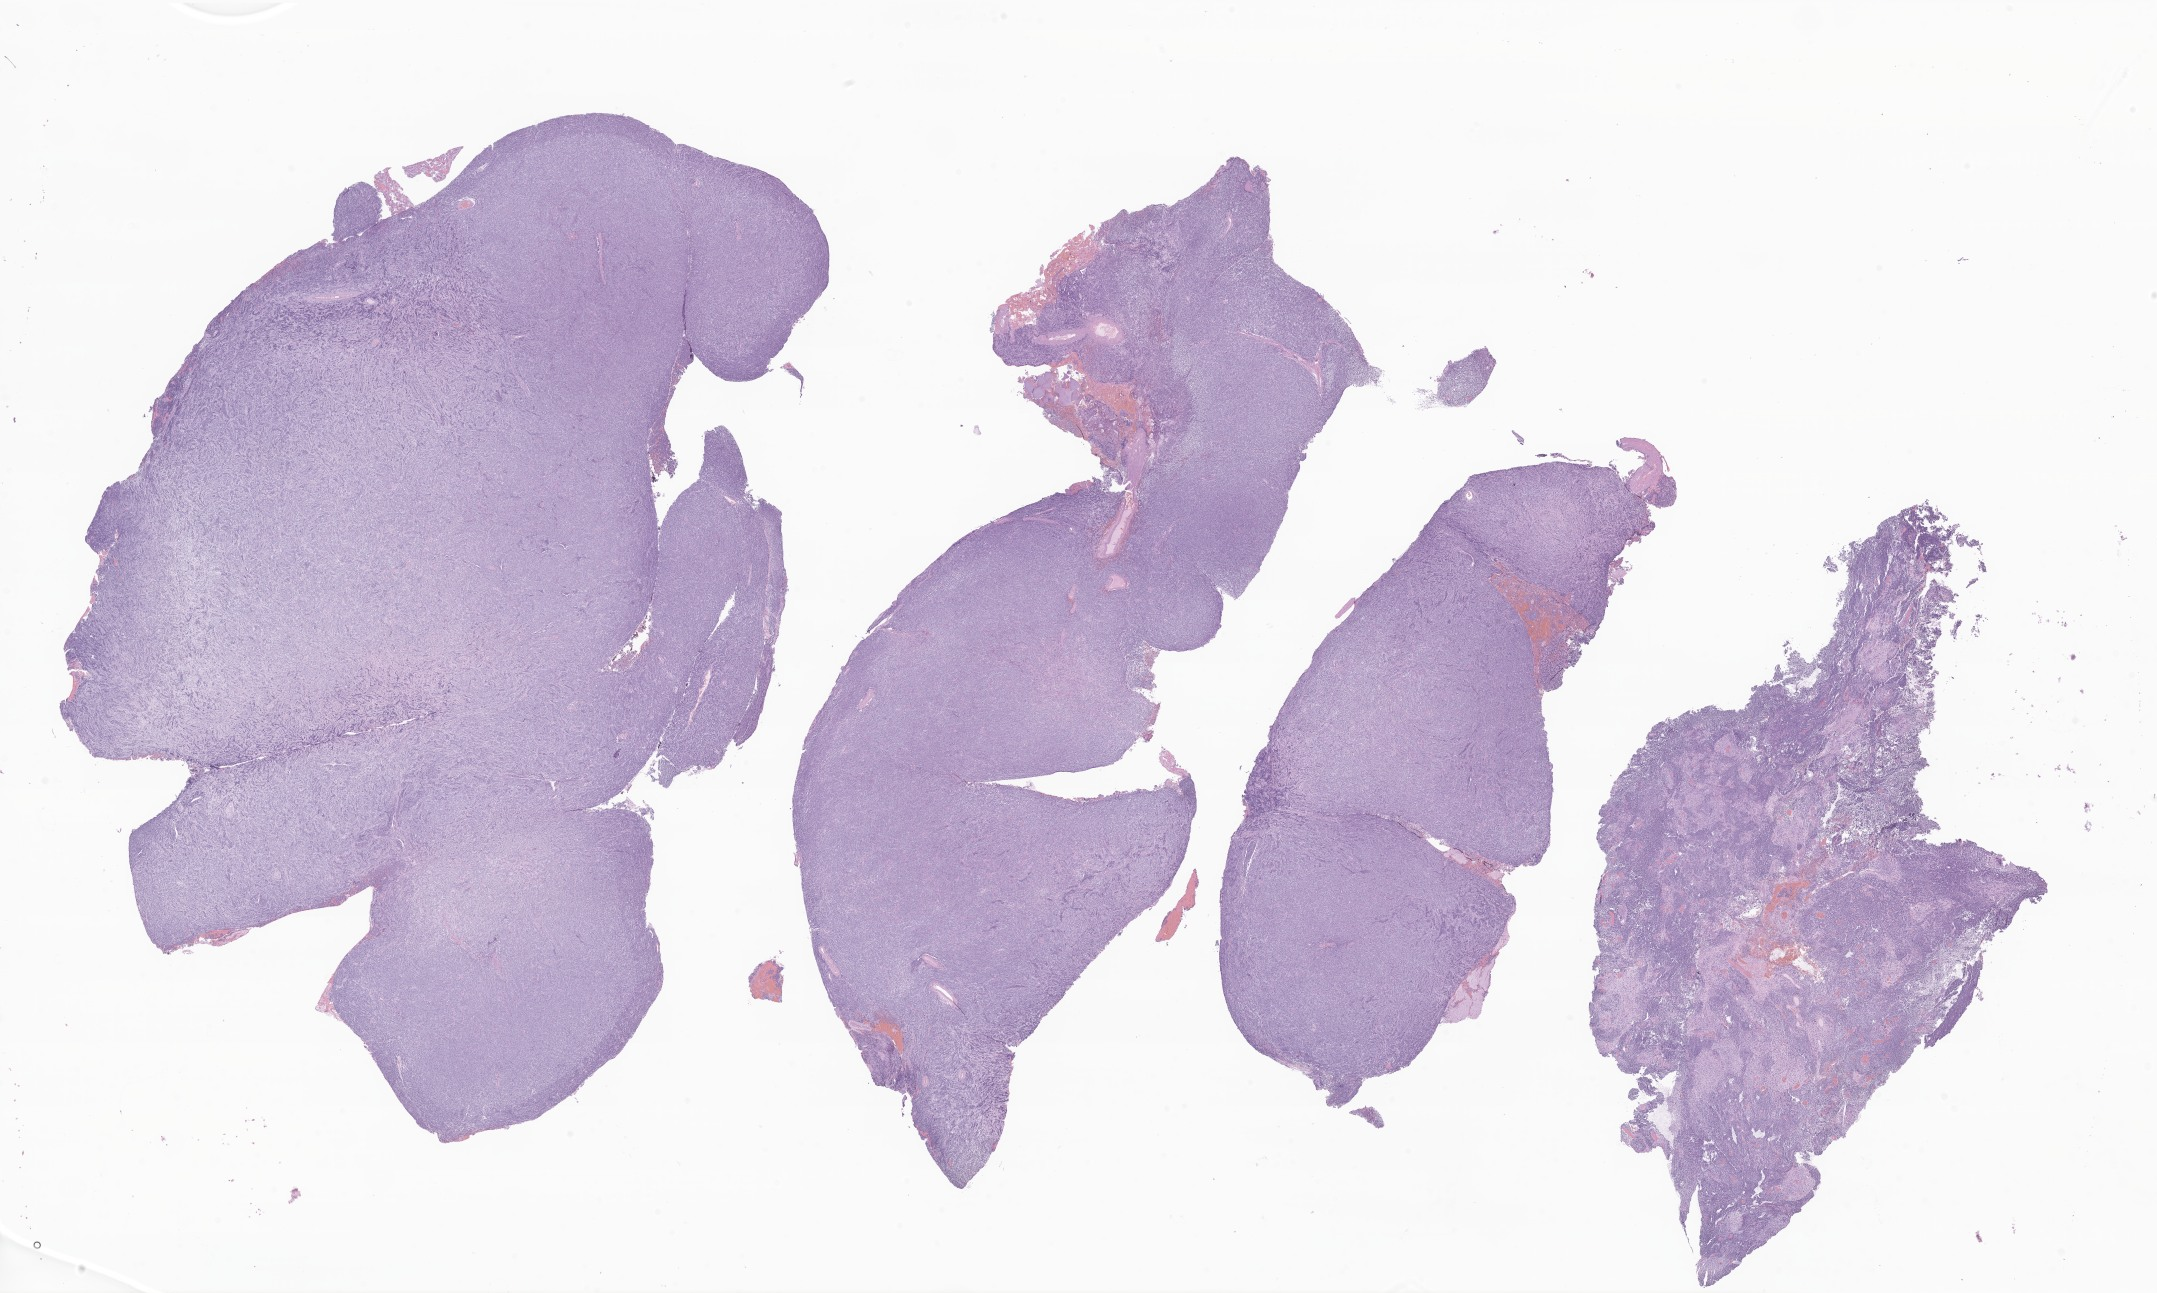
Digitized H&E-stained section of tumor tissue from the cerebral ventricle, low-resolution overview of the scanned area, about 36.4 x 21.8 mm, formalin-fixed, paraffin-embedded (FFPE) tissue. Patient male; age 64 months (5 years 4 months).
Diagnosis: Neoplasm, uncertain whether benign or malignant.